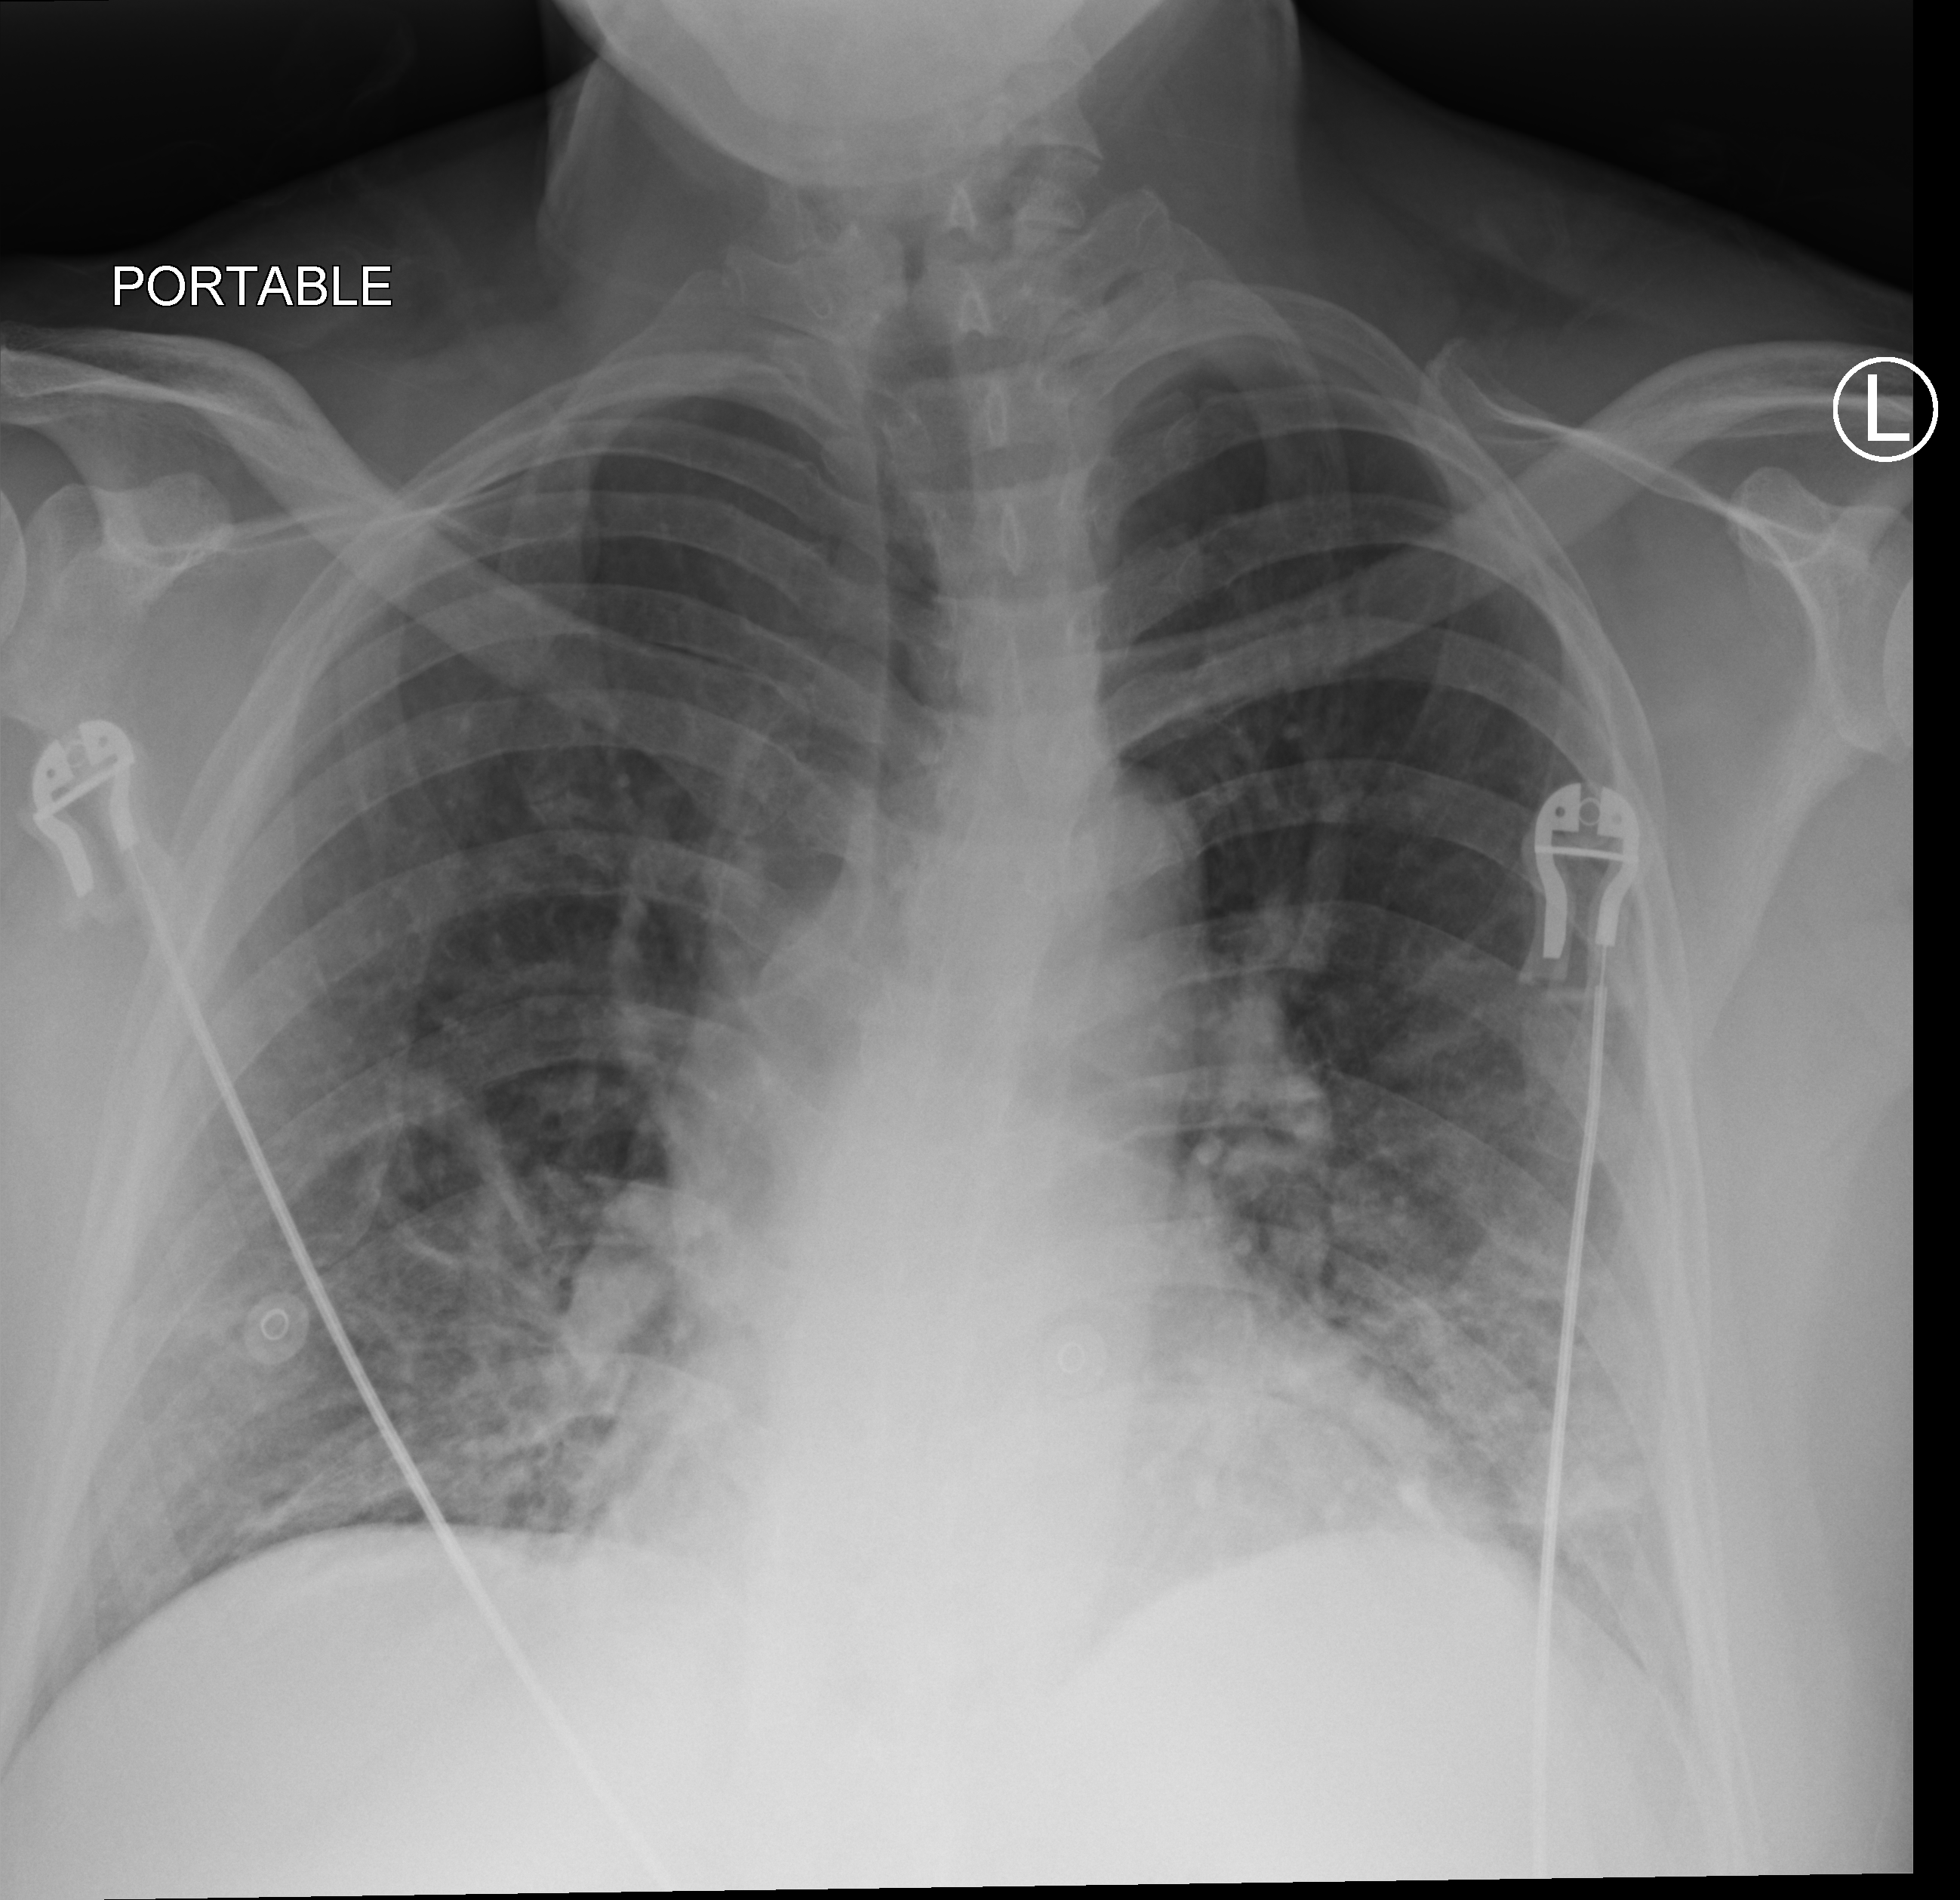
Chest X-ray (portable); anteroposterior (AP) projection. Patient hospitalised with COVID-19; male, aged 18–59 years.
Hospital-stay facts (about this admission, not read from this image; timing relative to this image not recorded):
- admitted to intensive care during this hospital stay: no
- mechanically ventilated during this hospital stay: no
- diabetes (admission record): no